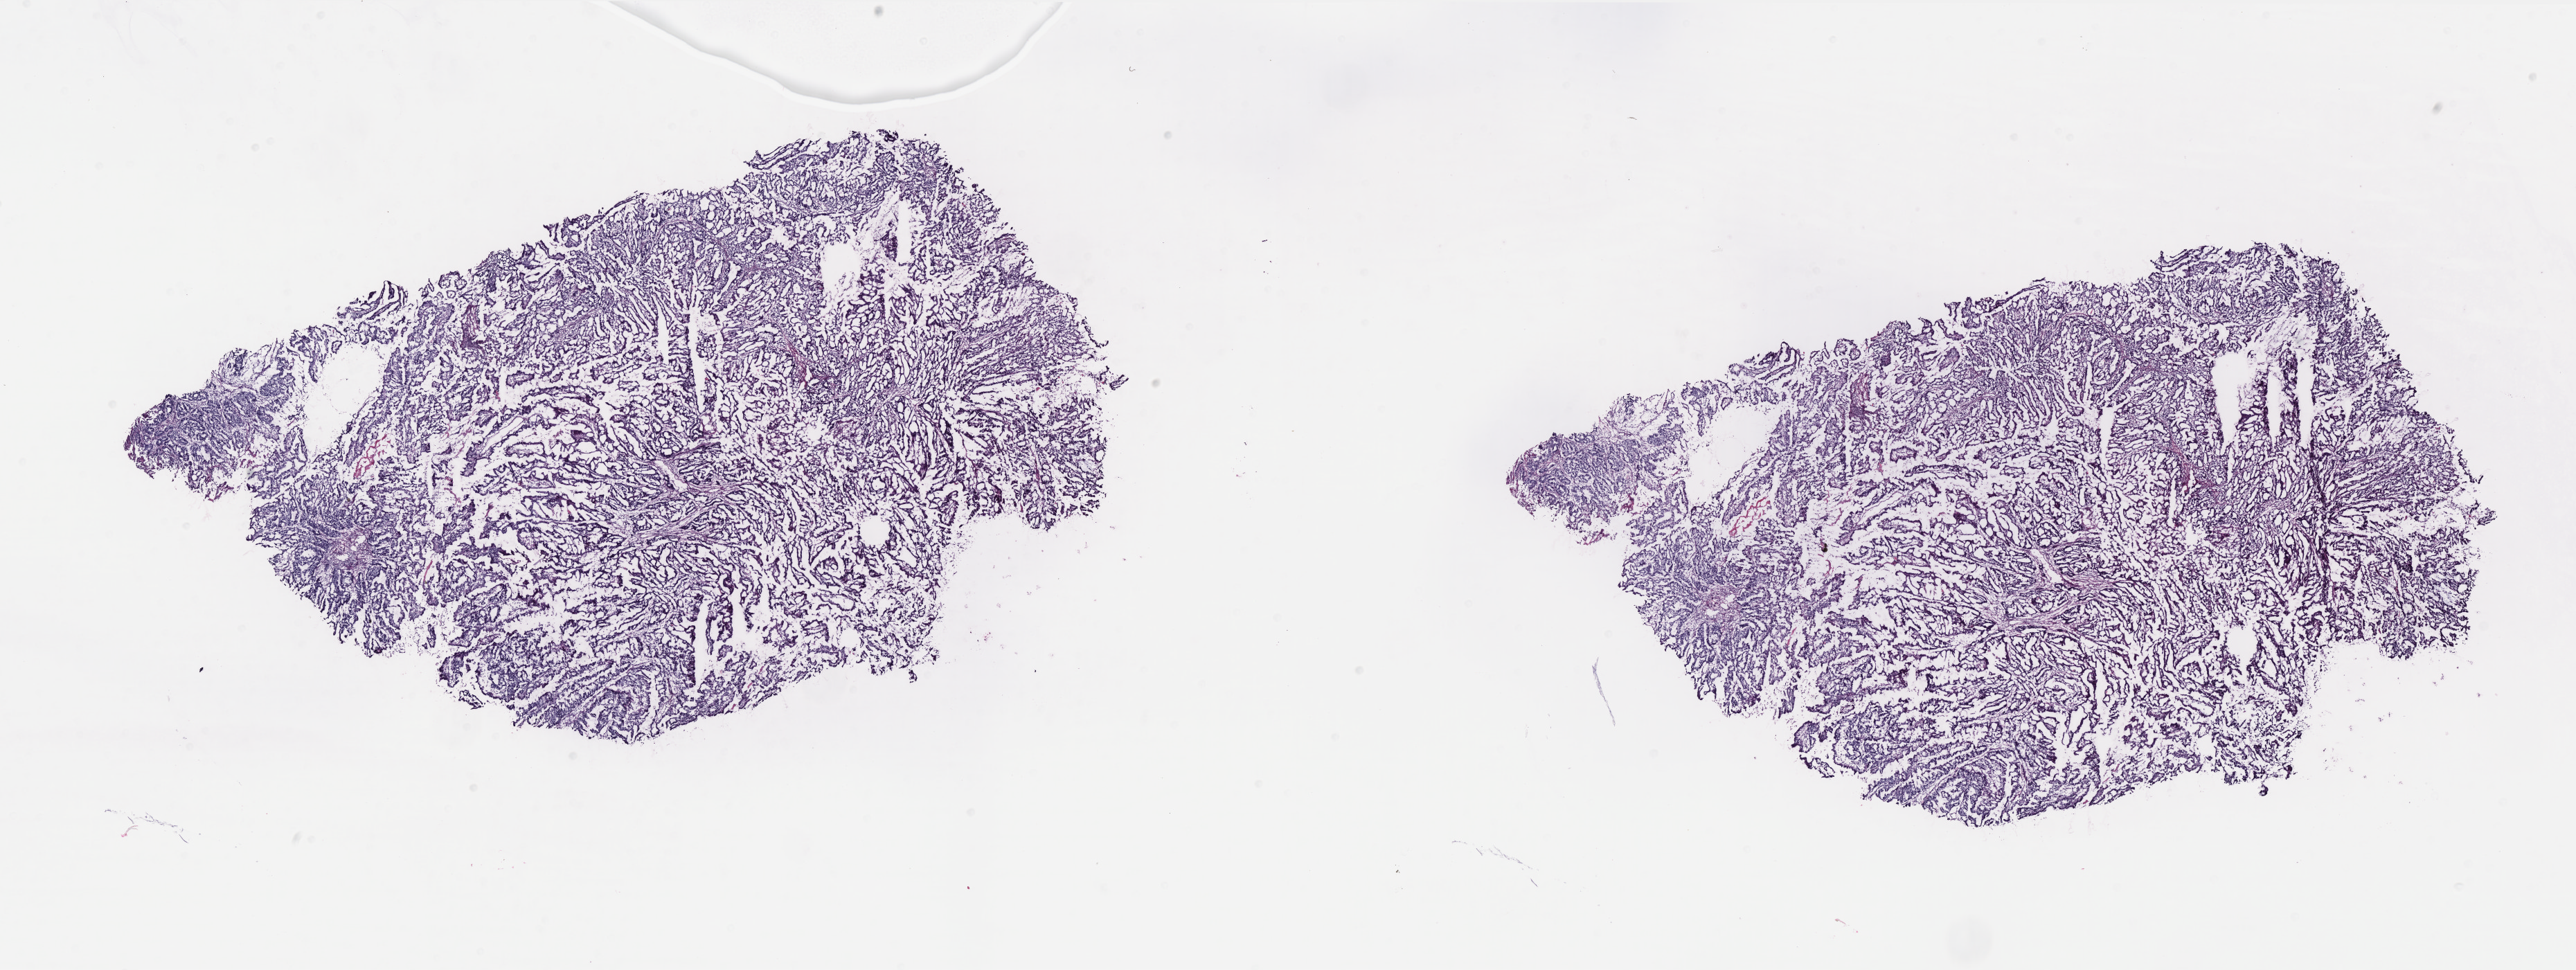
Whole-slide histology image, H&E, whole scanned area (about 29.8 x 11.2 mm) shown as a low-resolution overview. Frozen section. Primary tumour sample from the uterus. Female, age 73 years at initial diagnosis. Histologic grade: G2 (moderately differentiated). Pathologist review of this section (percent, as recorded): tumour cells 100%, tumour nuclei 80%, normal cells 0%, stromal cells 0%, necrosis 0%. Infiltration values recorded for this section: lymphocyte infiltration 0%, monocyte infiltration 0%, neutrophil infiltration 0%.
Pathologic diagnosis: Endometrioid adenocarcinoma, NOS (endometrium). FIGO stage: IB.